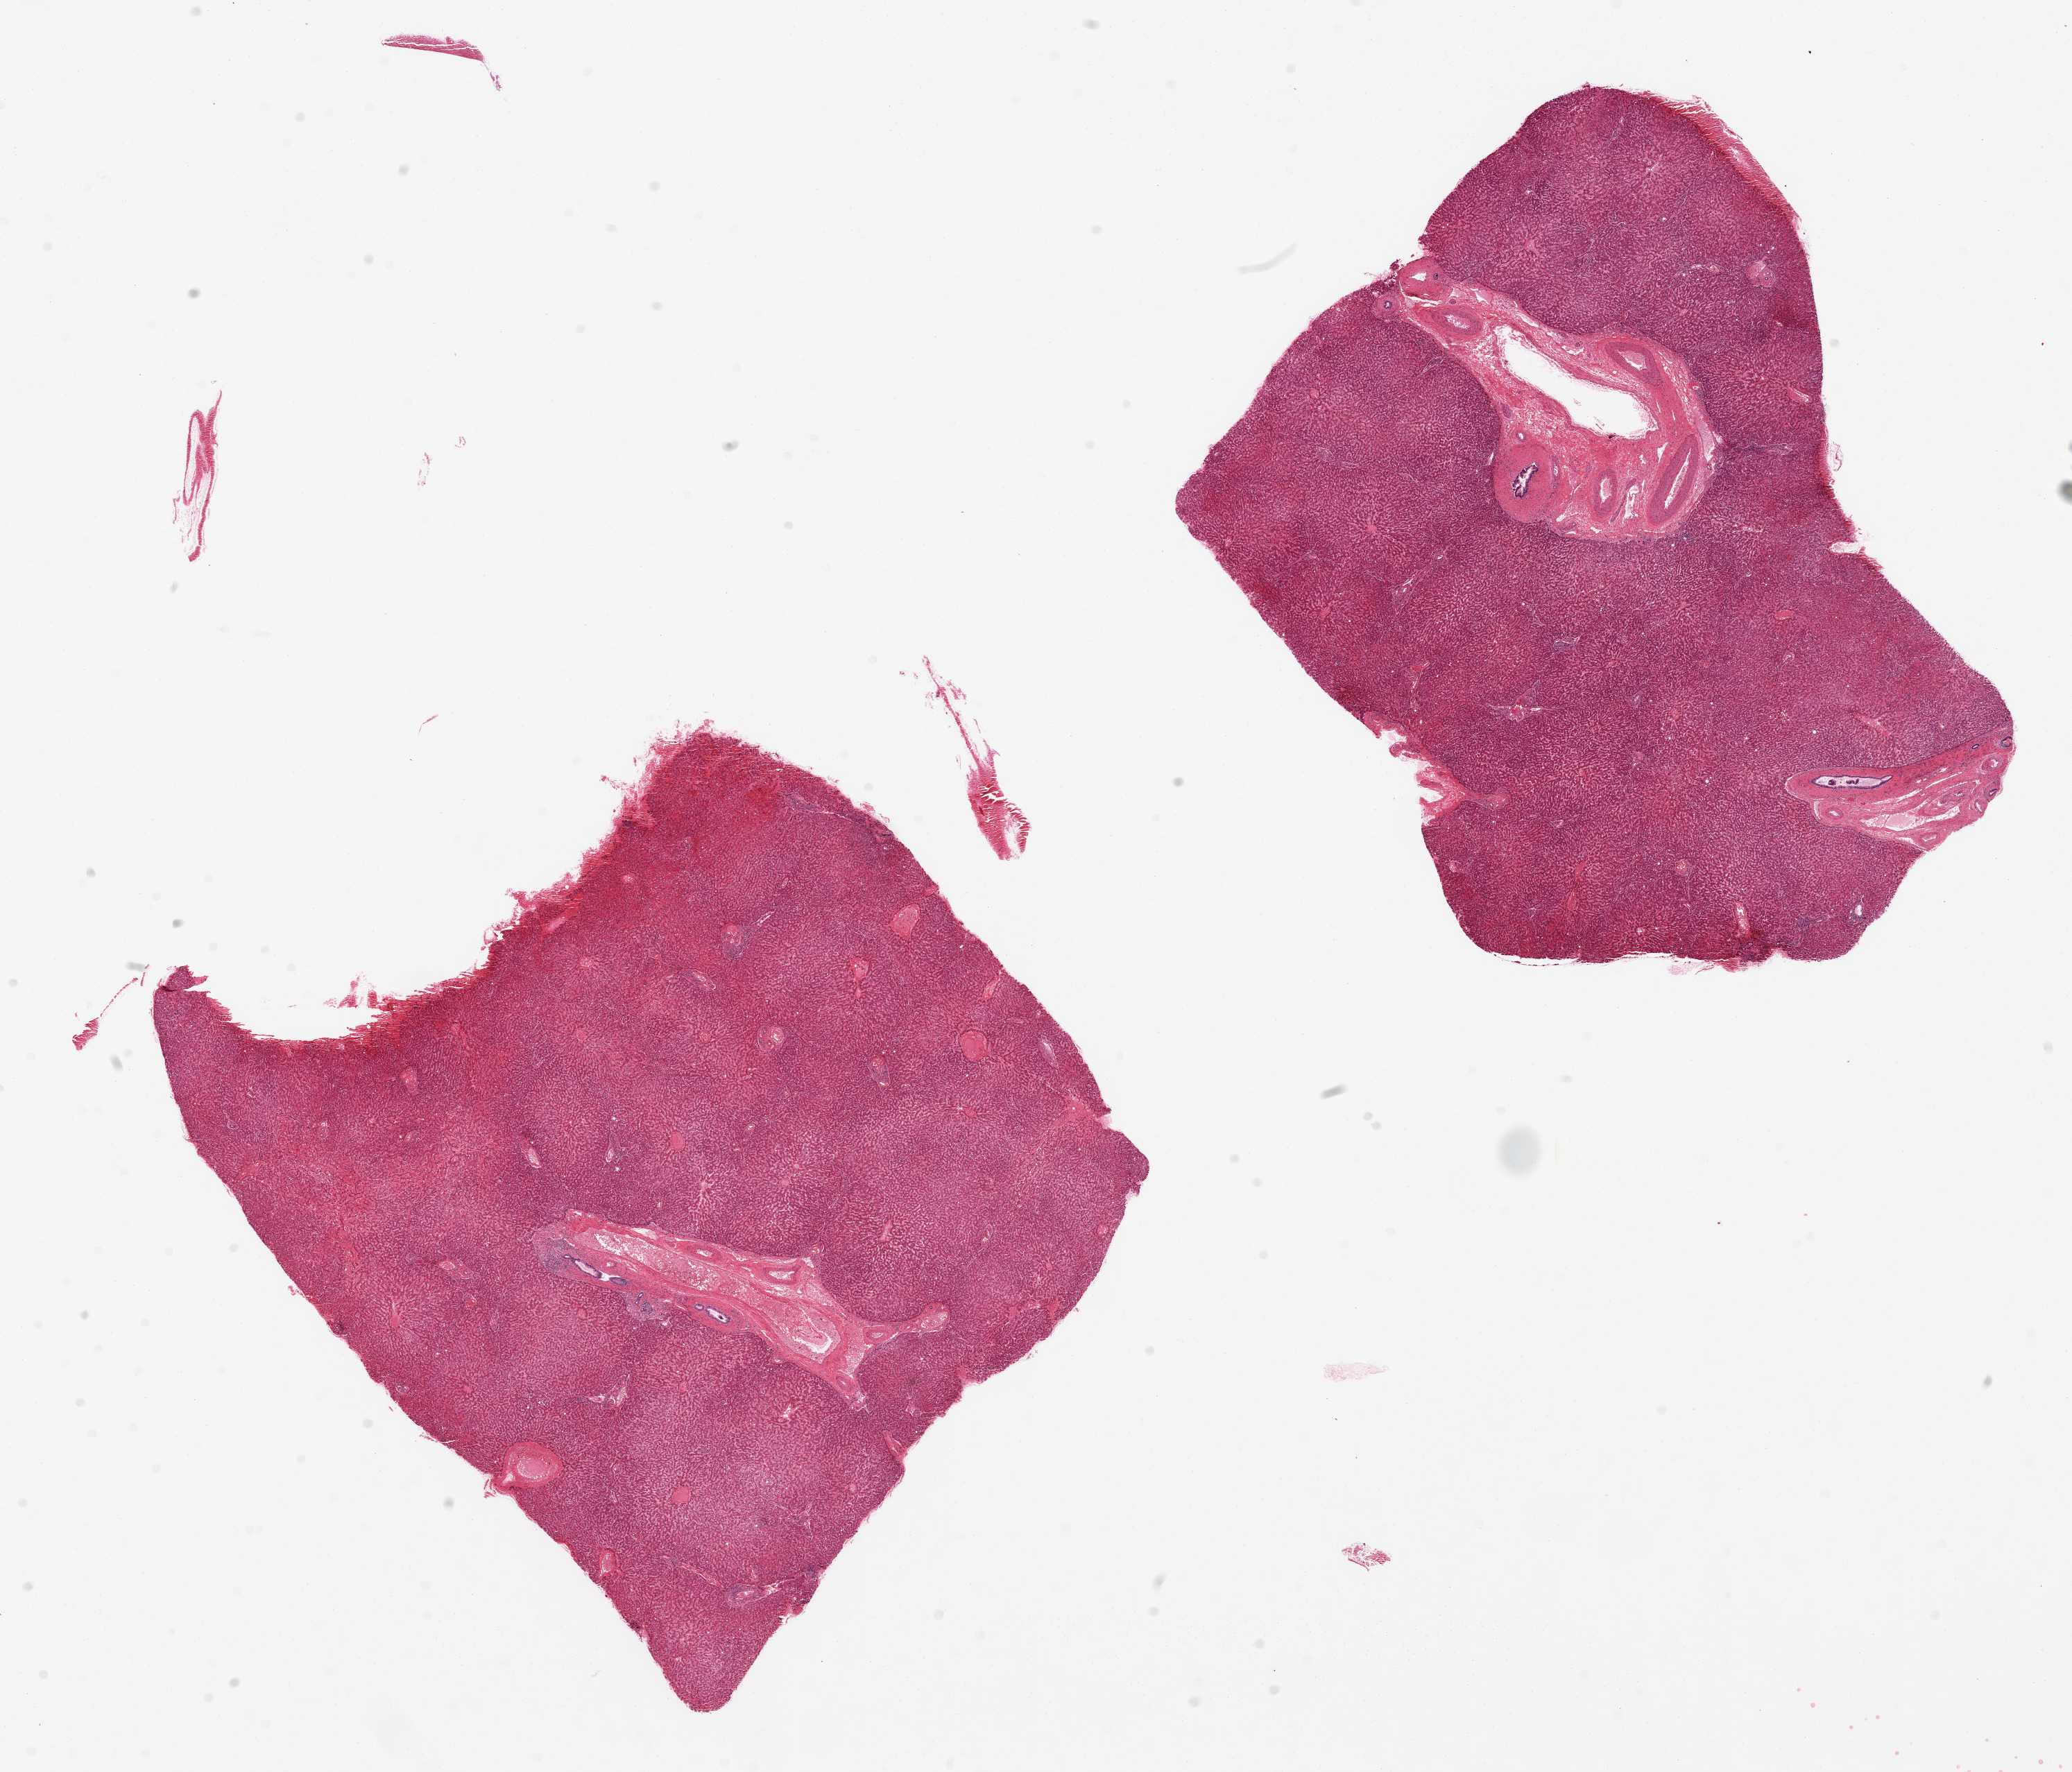
Whole-slide image, haematoxylin and eosin stain, brightfield — whole scanned area (about 23.6 x 20.2 mm, acquisition: 20x scan) shown as a low-resolution overview; PAXgene-fixed, paraffin-embedded tissue; sampled site (target tissue): liver; donor tissue sample. Donor sex: female.
Reviewer comment on this tissue sample: 2 pieces; mild macrovesicular steatosis.